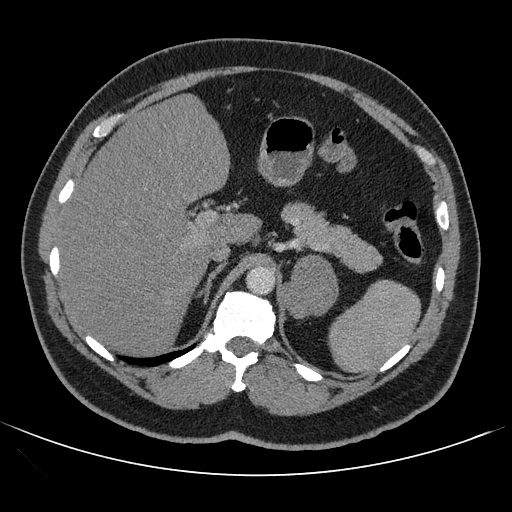
Contrast-enhanced abdominal CT, one axial slice; slice 74 of 121 in the series (ordered by position); 120 kVp; intravenous contrast given; soft-tissue window (W 400 / L 40 HU); 512 × 512 image matrix, field of view 399 × 399 mm. Patient: male, 53 years. From the clinical record (not read from this slice): diagnosis: adrenocortical carcinoma; tumour side: left adrenal; tumour size at pathology: 7.9 cm; Ki-67 index: 20 %; stage (as recorded): 2.
Structures marked on this image (semi-automatically segmented with operator editing):
- mass: bounding box <283,257,338,317> (left, top, right, bottom; pixels)